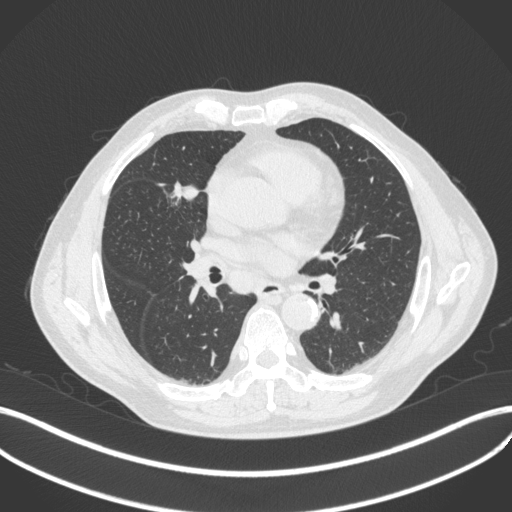
Chest CT, one axial slice. Reconstruction kernel B31f. 120 kVp. Lung window (W 1500 / L -600 HU). 512 × 512 image matrix, field of view 400 × 400 mm. Patient: male, 61 years. Case-level facts recorded for this patient, not image findings: clinical TNM (as recorded): T2b N1 M0.
Outlined on this slice (bounding box drawn by a radiologist):
- lung tumour (recorded histology: squamous cell carcinoma): bounding box (x1, y1, x2, y2) in pixels: (173, 181, 200, 208)